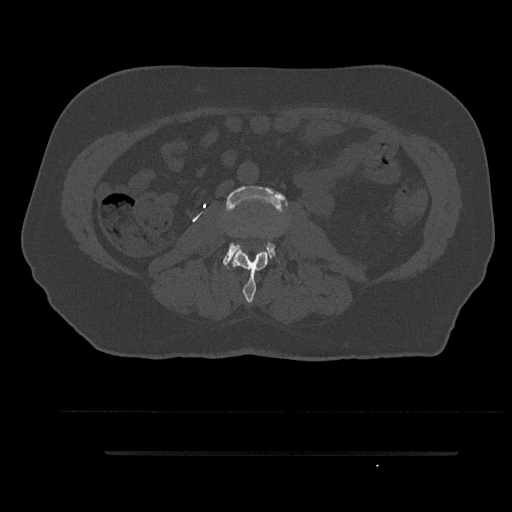
CT including the spine, one axial slice. Slice 75 of 797 in the series (ordered by position). 120 kVp. Bone window (W 1800 / L 400 HU). 0.5 mm slice thickness. 512 × 512 image matrix, field of view 432 × 432 mm. Patient: male, 63 years. Case-level facts recorded for this patient, not image findings: primary cancer: renal.
Structures marked on this image (semi-automatic segmentation, software-assisted and operator-edited):
- L2 vertebra: box from (x=232, y=250) to (x=268, y=303) px
- L3 vertebra: (x=223, y=185)–(x=287, y=267)